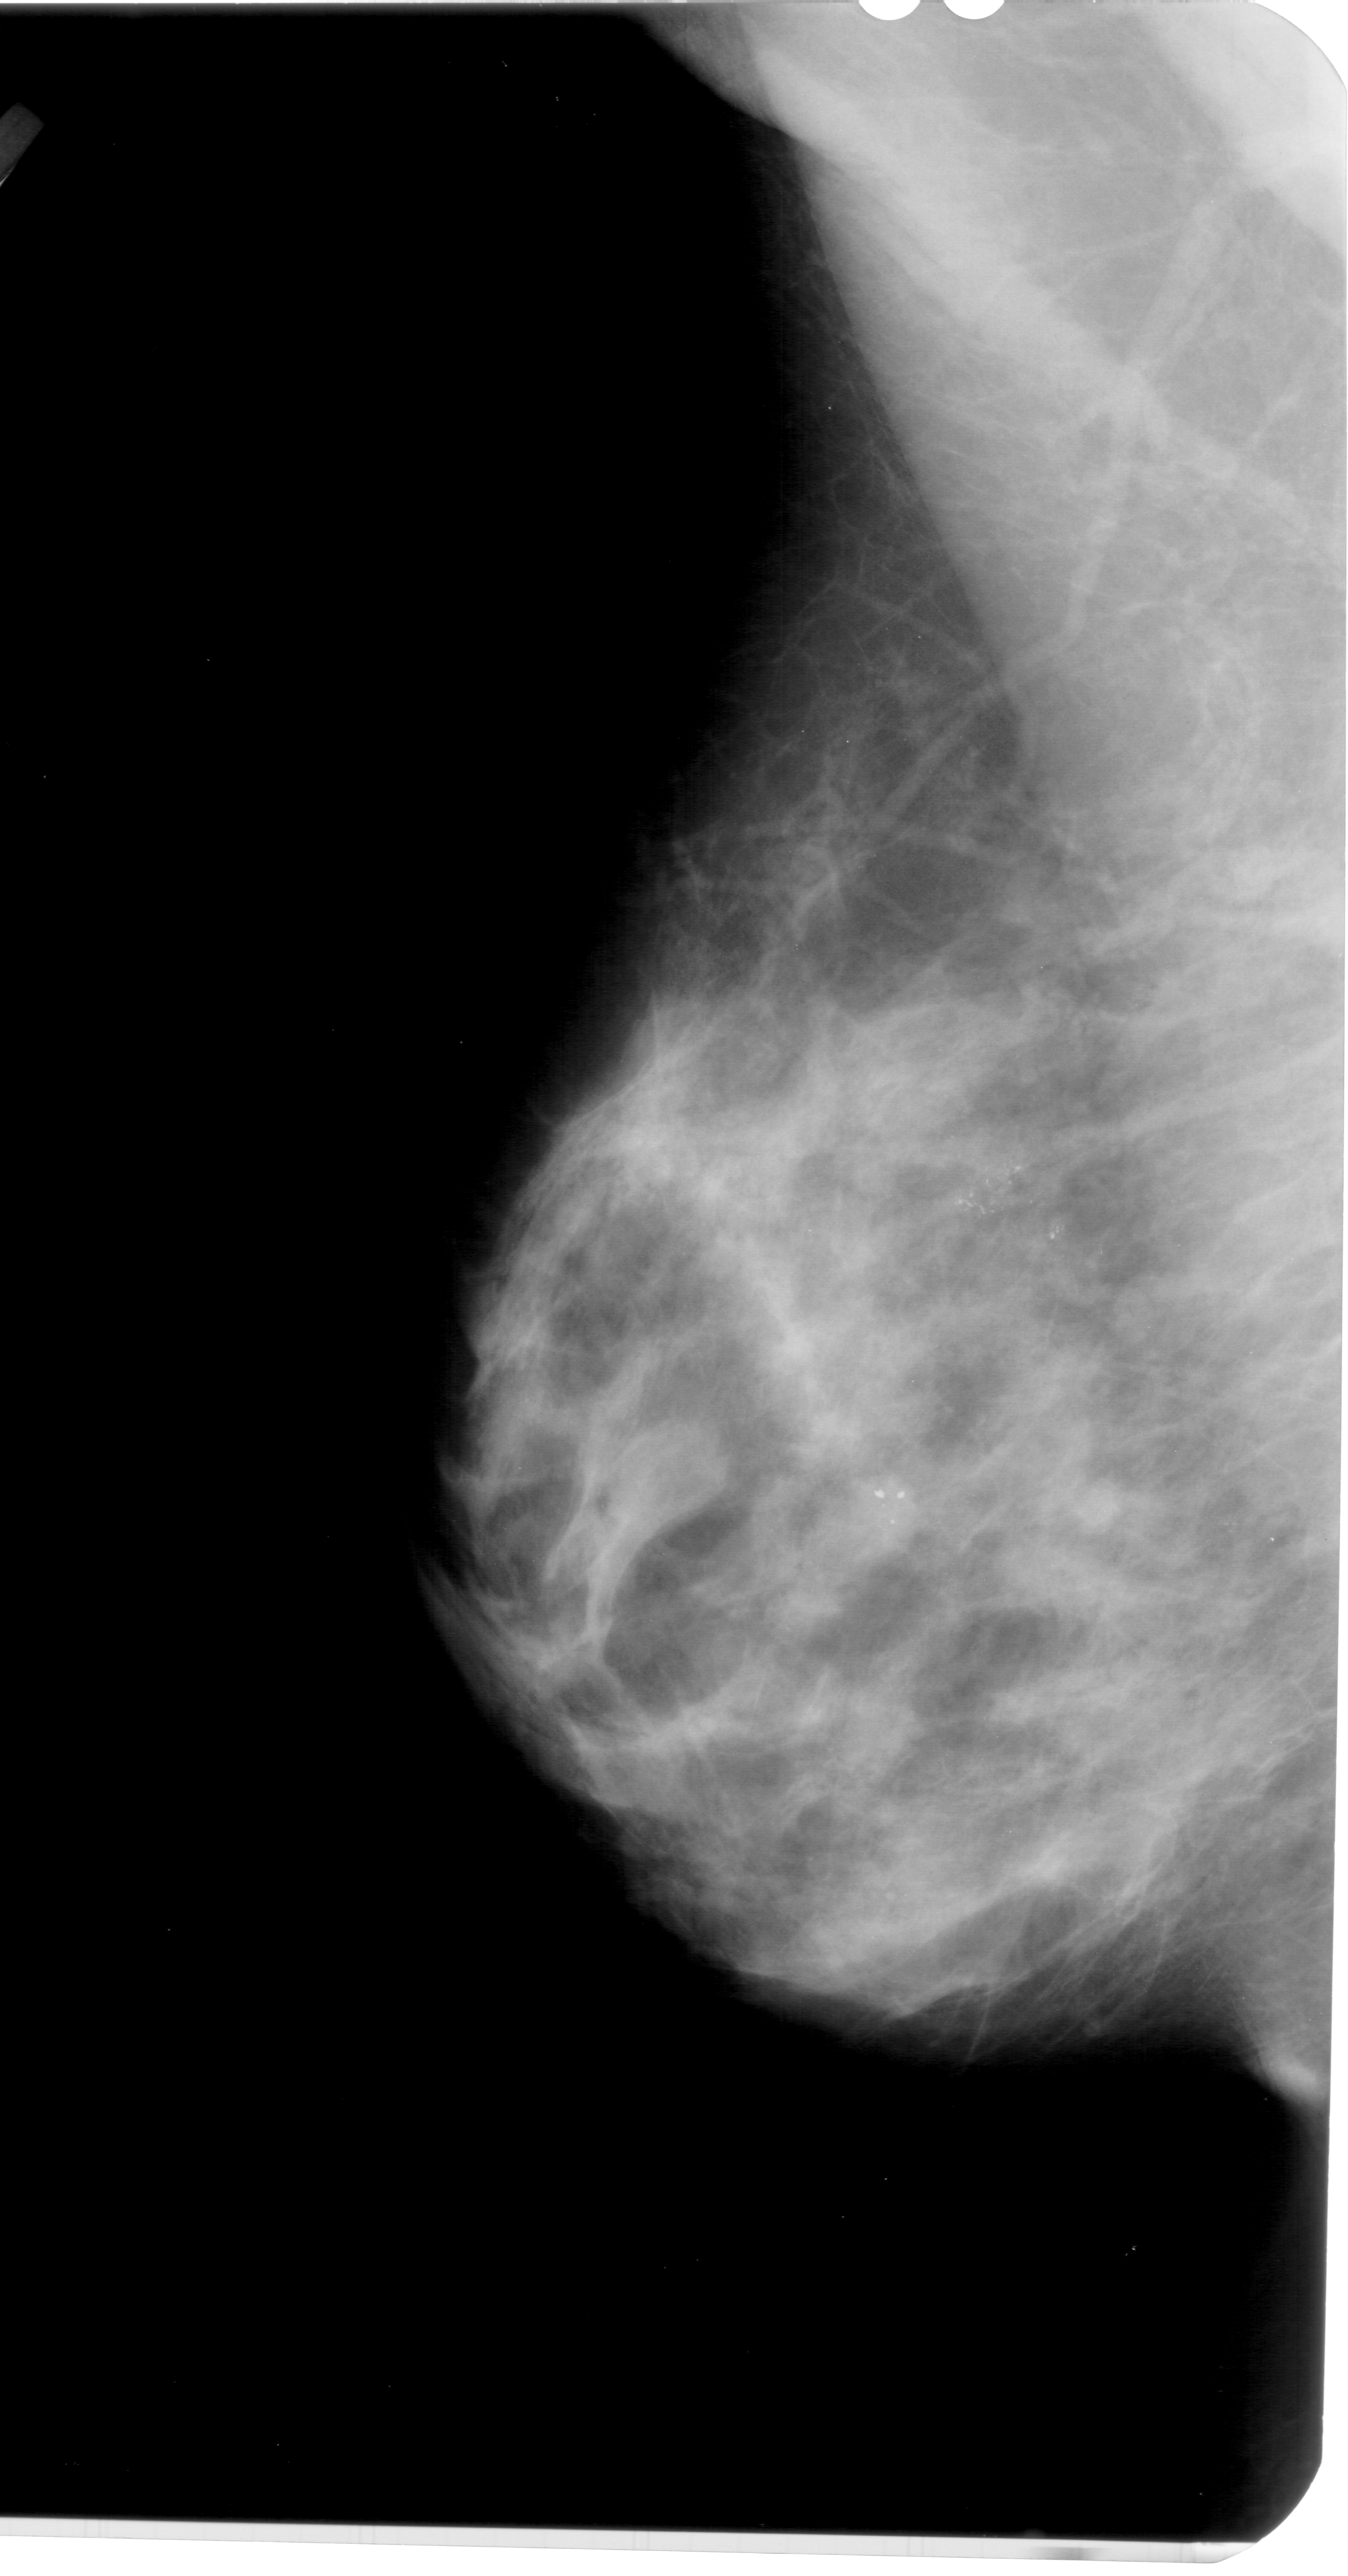
Digitized screen-film mammogram, left breast, mediolateral oblique (MLO) view, BI-RADS breast density category 4 (scale 1–4).
Marked findings (only marked abnormalities are described; nothing is implied about the rest of the image): calcifications, morphology pleomorphic, distribution clustered; BI-RADS assessment category 4; pathology (as recorded): malignant.